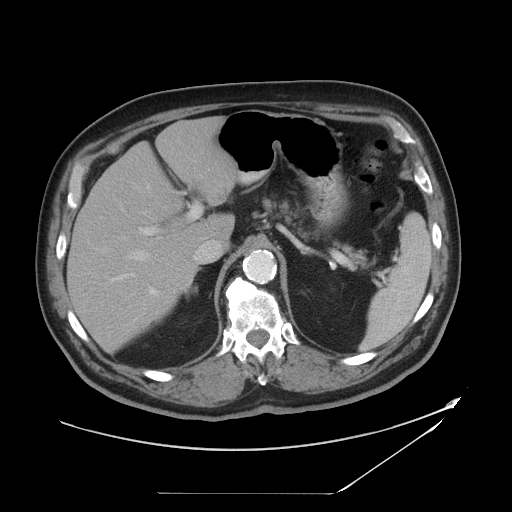
Contrast-enhanced abdominal CT, one axial slice; position 30 of 49 along the scan axis; intravenous contrast given; soft-tissue window (W 400 / L 40 HU); 512 × 512 image matrix, field of view 461 × 461 mm. Male patient, age 72 years. Case-level facts recorded for this patient, not image findings: diagnosis: colorectal cancer liver metastases, imaged before liver resection; multiple liver metastases: no; largest metastasis: 2.5 cm; disease in both lobes: no.
Outlined on this slice (outlined manually by an expert reader):
- hepatic veins: bounding box (x1, y1, x2, y2) in pixels: (127, 182, 151, 261)
- liver: (68, 120, 232, 349)
- planned liver remnant (the part of the liver to remain after resection): (68, 169, 196, 349)
- portal vein (with intrahepatic branches): (110, 203, 202, 296)
- liver metastasis: (210, 182, 229, 201)